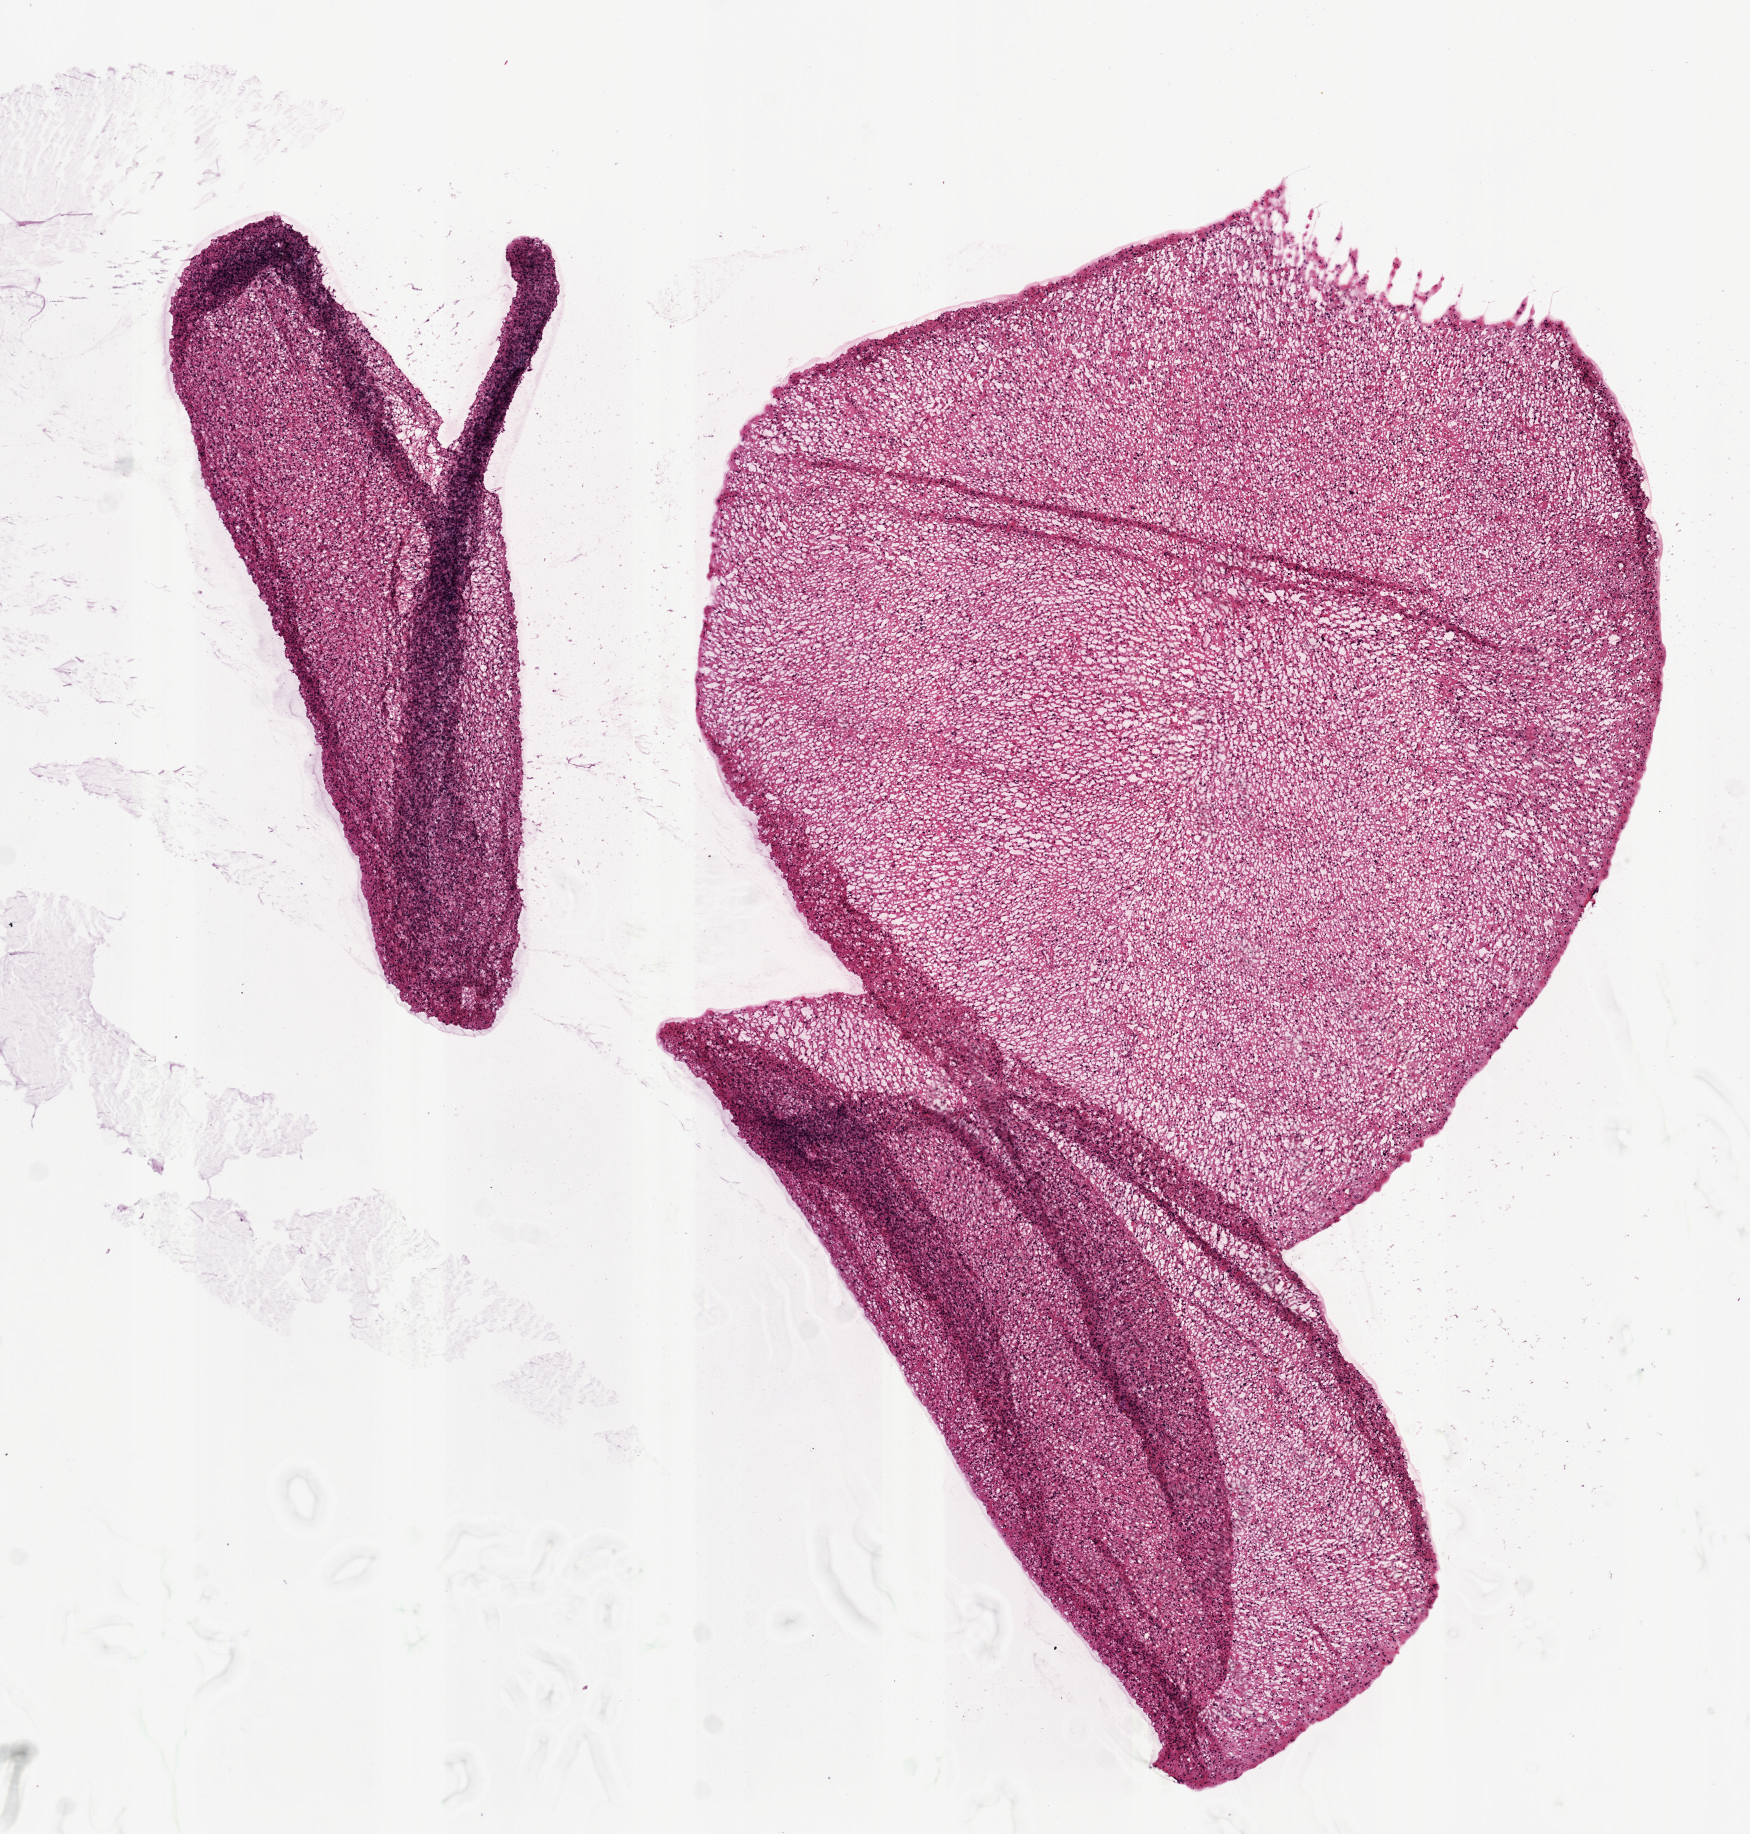
Hematoxylin and eosin (H&E) stained whole-slide image, whole scanned area (about 7.0 x 7.4 mm, slide scanned at 20x) shown as a low-resolution overview, frozen section, primary tumour sample from the brain. Patient: male, age at initial diagnosis 29 years.
Pathologic diagnosis: Astrocytoma, anaplastic.